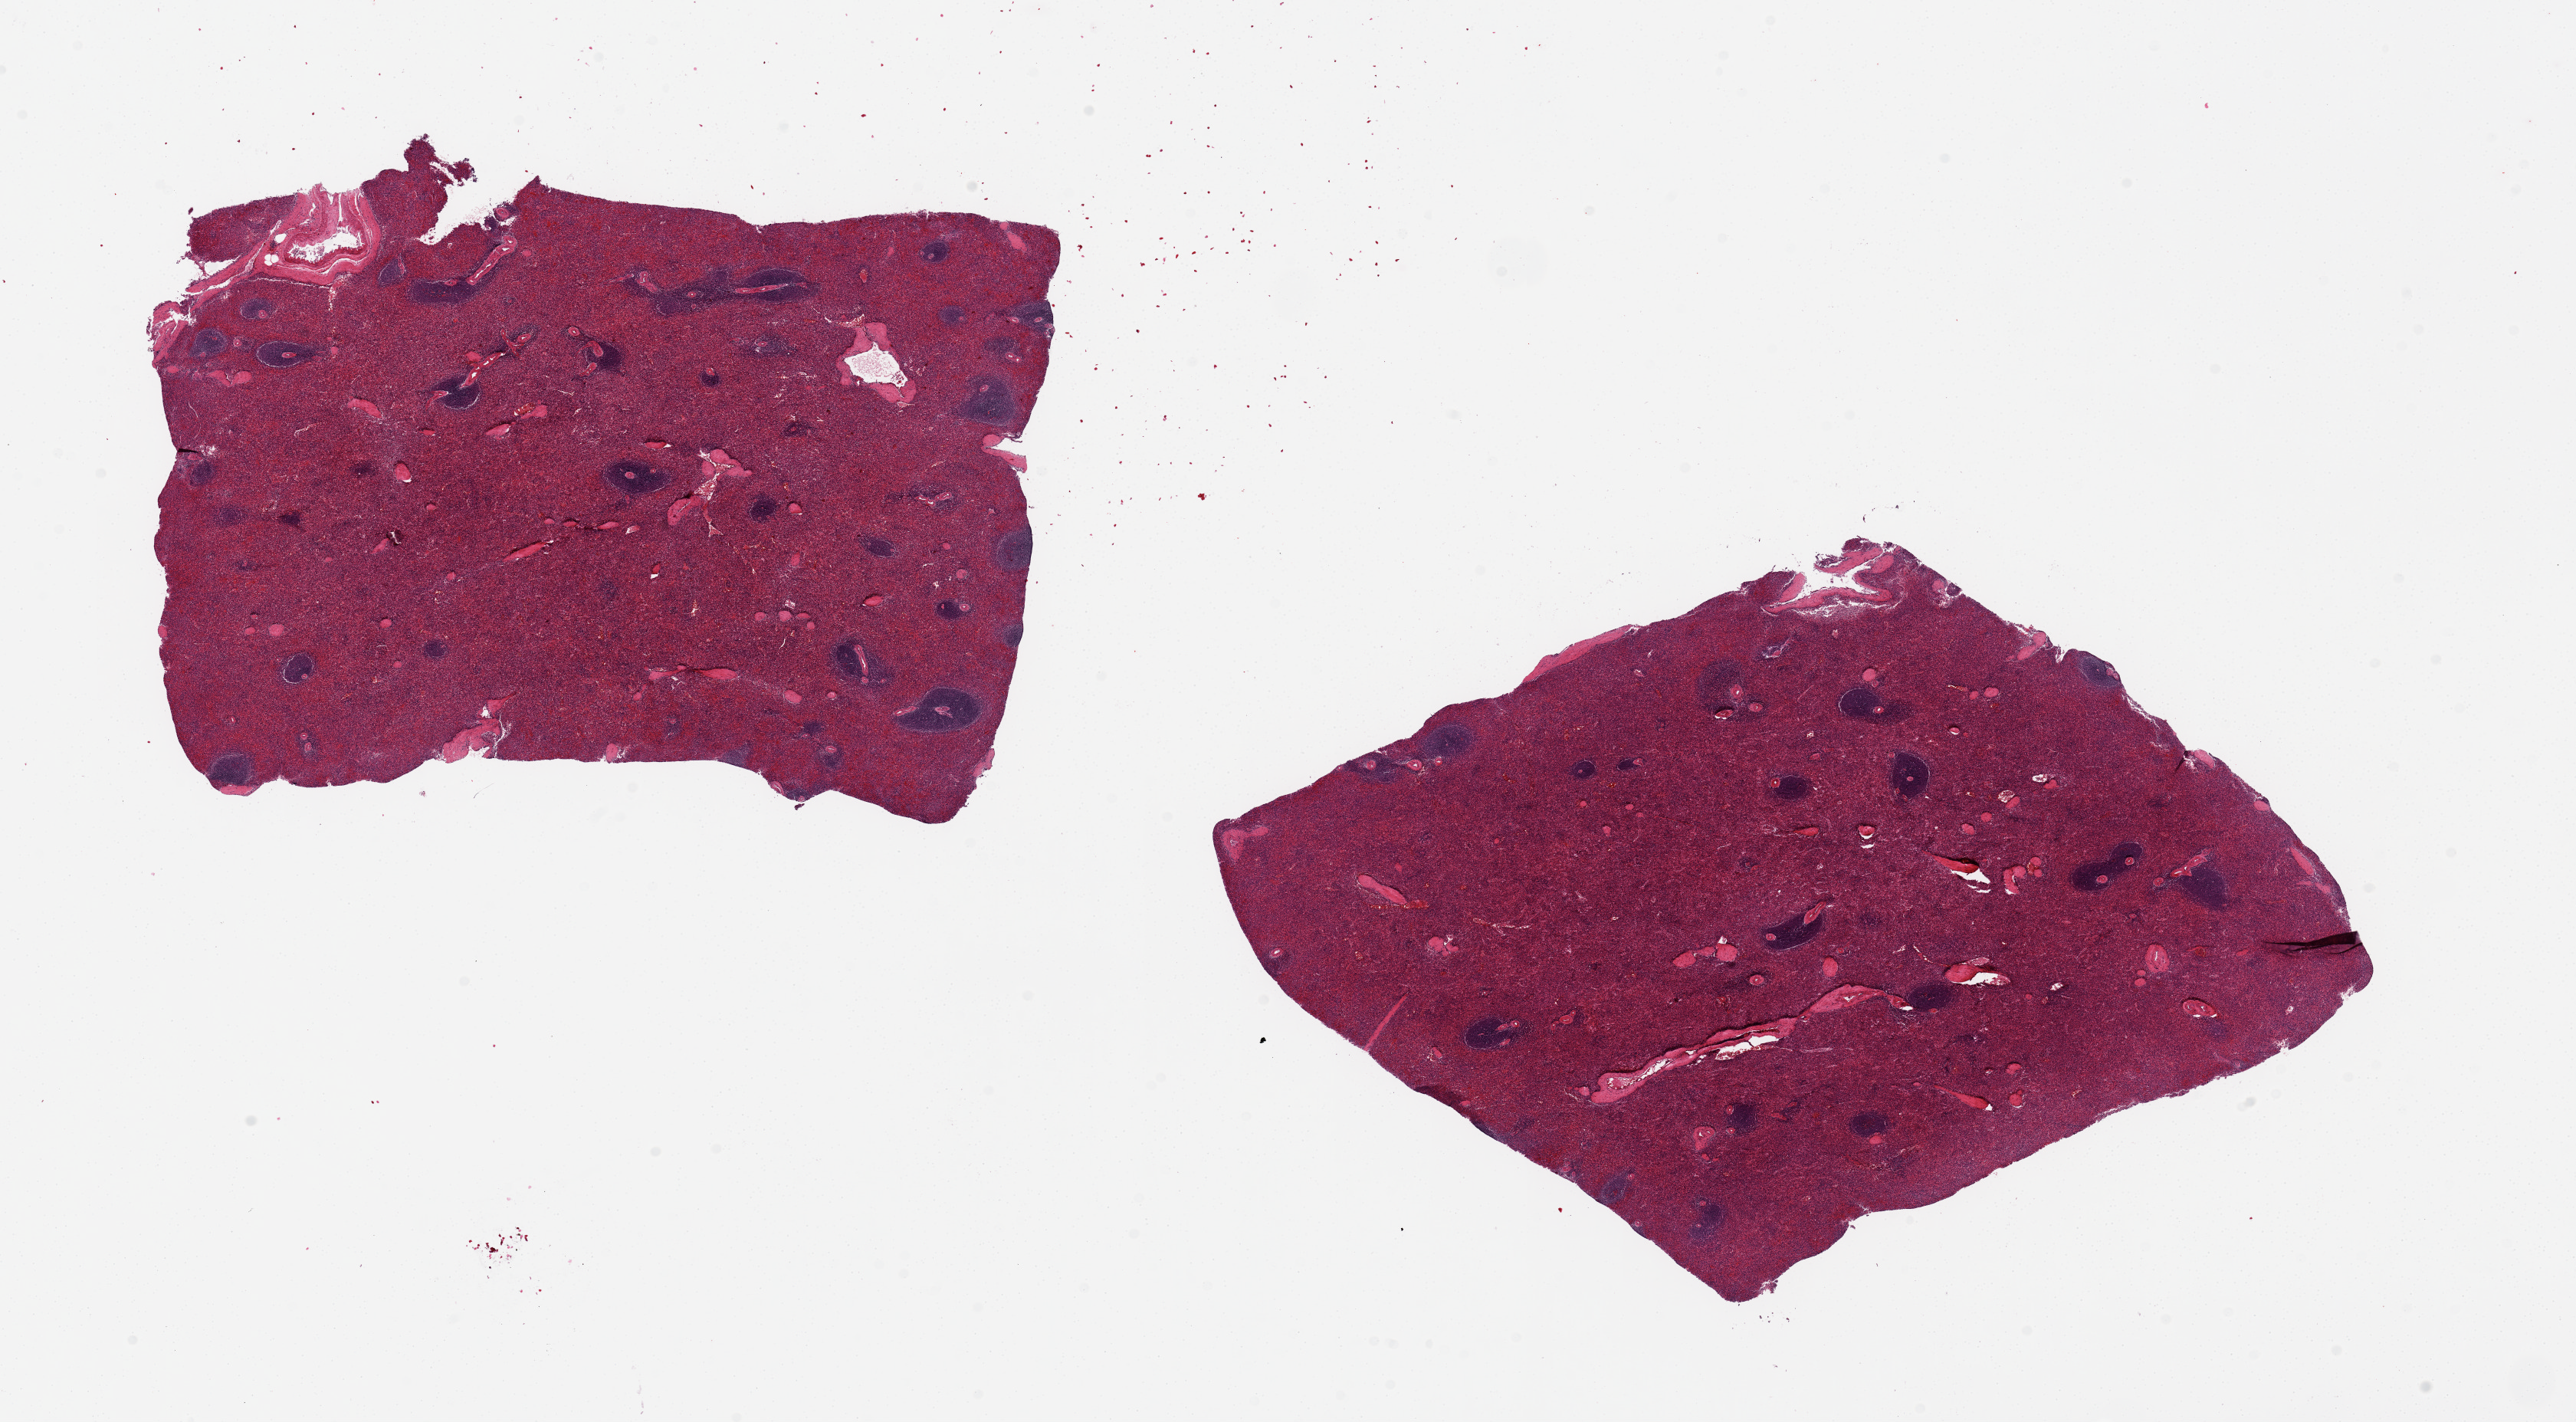
Whole-slide image, H&E stain, low-resolution overview of the scanned area, about 26.6 x 14.7 mm; PAXgene-fixed paraffin-embedded (PFPE) section; target tissue: spleen; donor tissue sample. Donor sex: male.
* pathologist's review note for this sample: 2 pieces, 9x6 and 8x7mm; moderate congestion